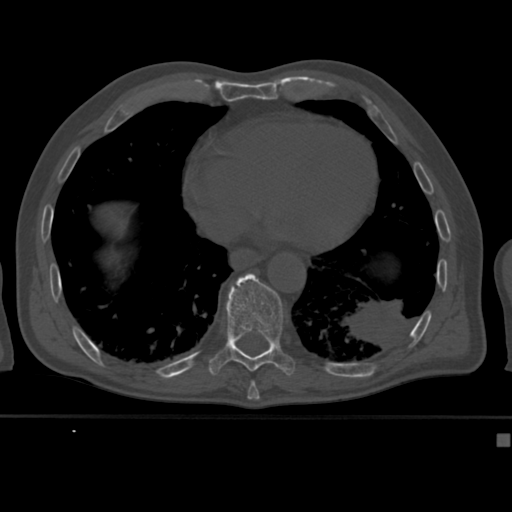
CT including the spine, one axial slice. Slice 230 of 430 in the series (ordered by position). Bone window (W 1800 / L 400 HU). 1.5 mm slice thickness. 512 × 512 image matrix, field of view 337 × 337 mm. Patient: male, 64 years. Case-level facts recorded for this patient, not image findings: primary cancer: uterus; vertebrae with lytic lesions (as recorded): T1, T4, T5, T7, L5.
Annotated regions visible in this slice (semi-automatically segmented with operator editing):
- T10 vertebra: bounding box (x1, y1, x2, y2) in pixels: (208, 273, 296, 377)
- T9 vertebra: (251, 380, 255, 382)